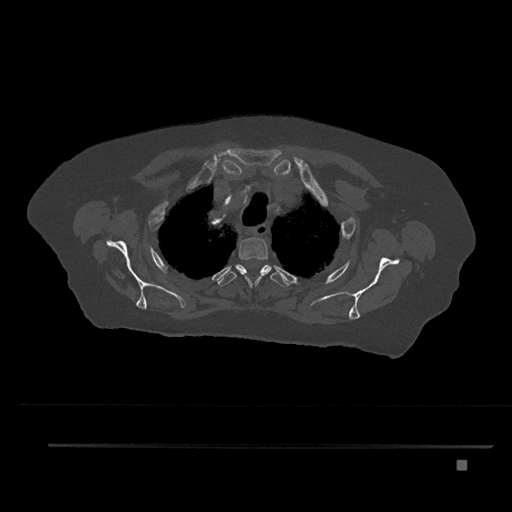
CT including the spine, one axial slice; bone window (W 1800 / L 400 HU); 0.5 mm slice thickness; 512 × 512 image matrix. Female patient, age 76 years. From the clinical record (not read from this slice): primary cancer: lung; vertebrae with lytic lesions (as recorded): T11, L3.
Outlined on this slice (semi-automatically segmented with operator editing):
- T2 vertebra: bounding box (x1, y1, x2, y2) in pixels: (235, 237, 271, 288)
- T3 vertebra: (218, 264, 289, 287)